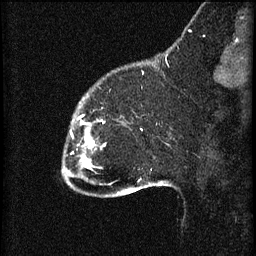
Breast MRI (dynamic contrast-enhanced), one sagittal slice; slice 12 of 60 in the series (ordered by position); 3 images stored at this slice position (order not interpretable as contrast timing); 1.5 T; TE 4.2 ms, TR 8.2 ms; 2 mm slice thickness; 256 × 256 image matrix. Female patient, age 32 years.
Structures marked on this image (semi-automatically segmented with operator editing):
- analysis volume of interest (the breast-tissue region the enhancement analysis was run in; not a lesion): bounding box [x1, y1, x2, y2] px = [63, 106, 106, 165]
- tumour enhancement mask (voxels above the 70 % enhancement threshold inside the analysis volume of interest): [83, 138, 93, 165]